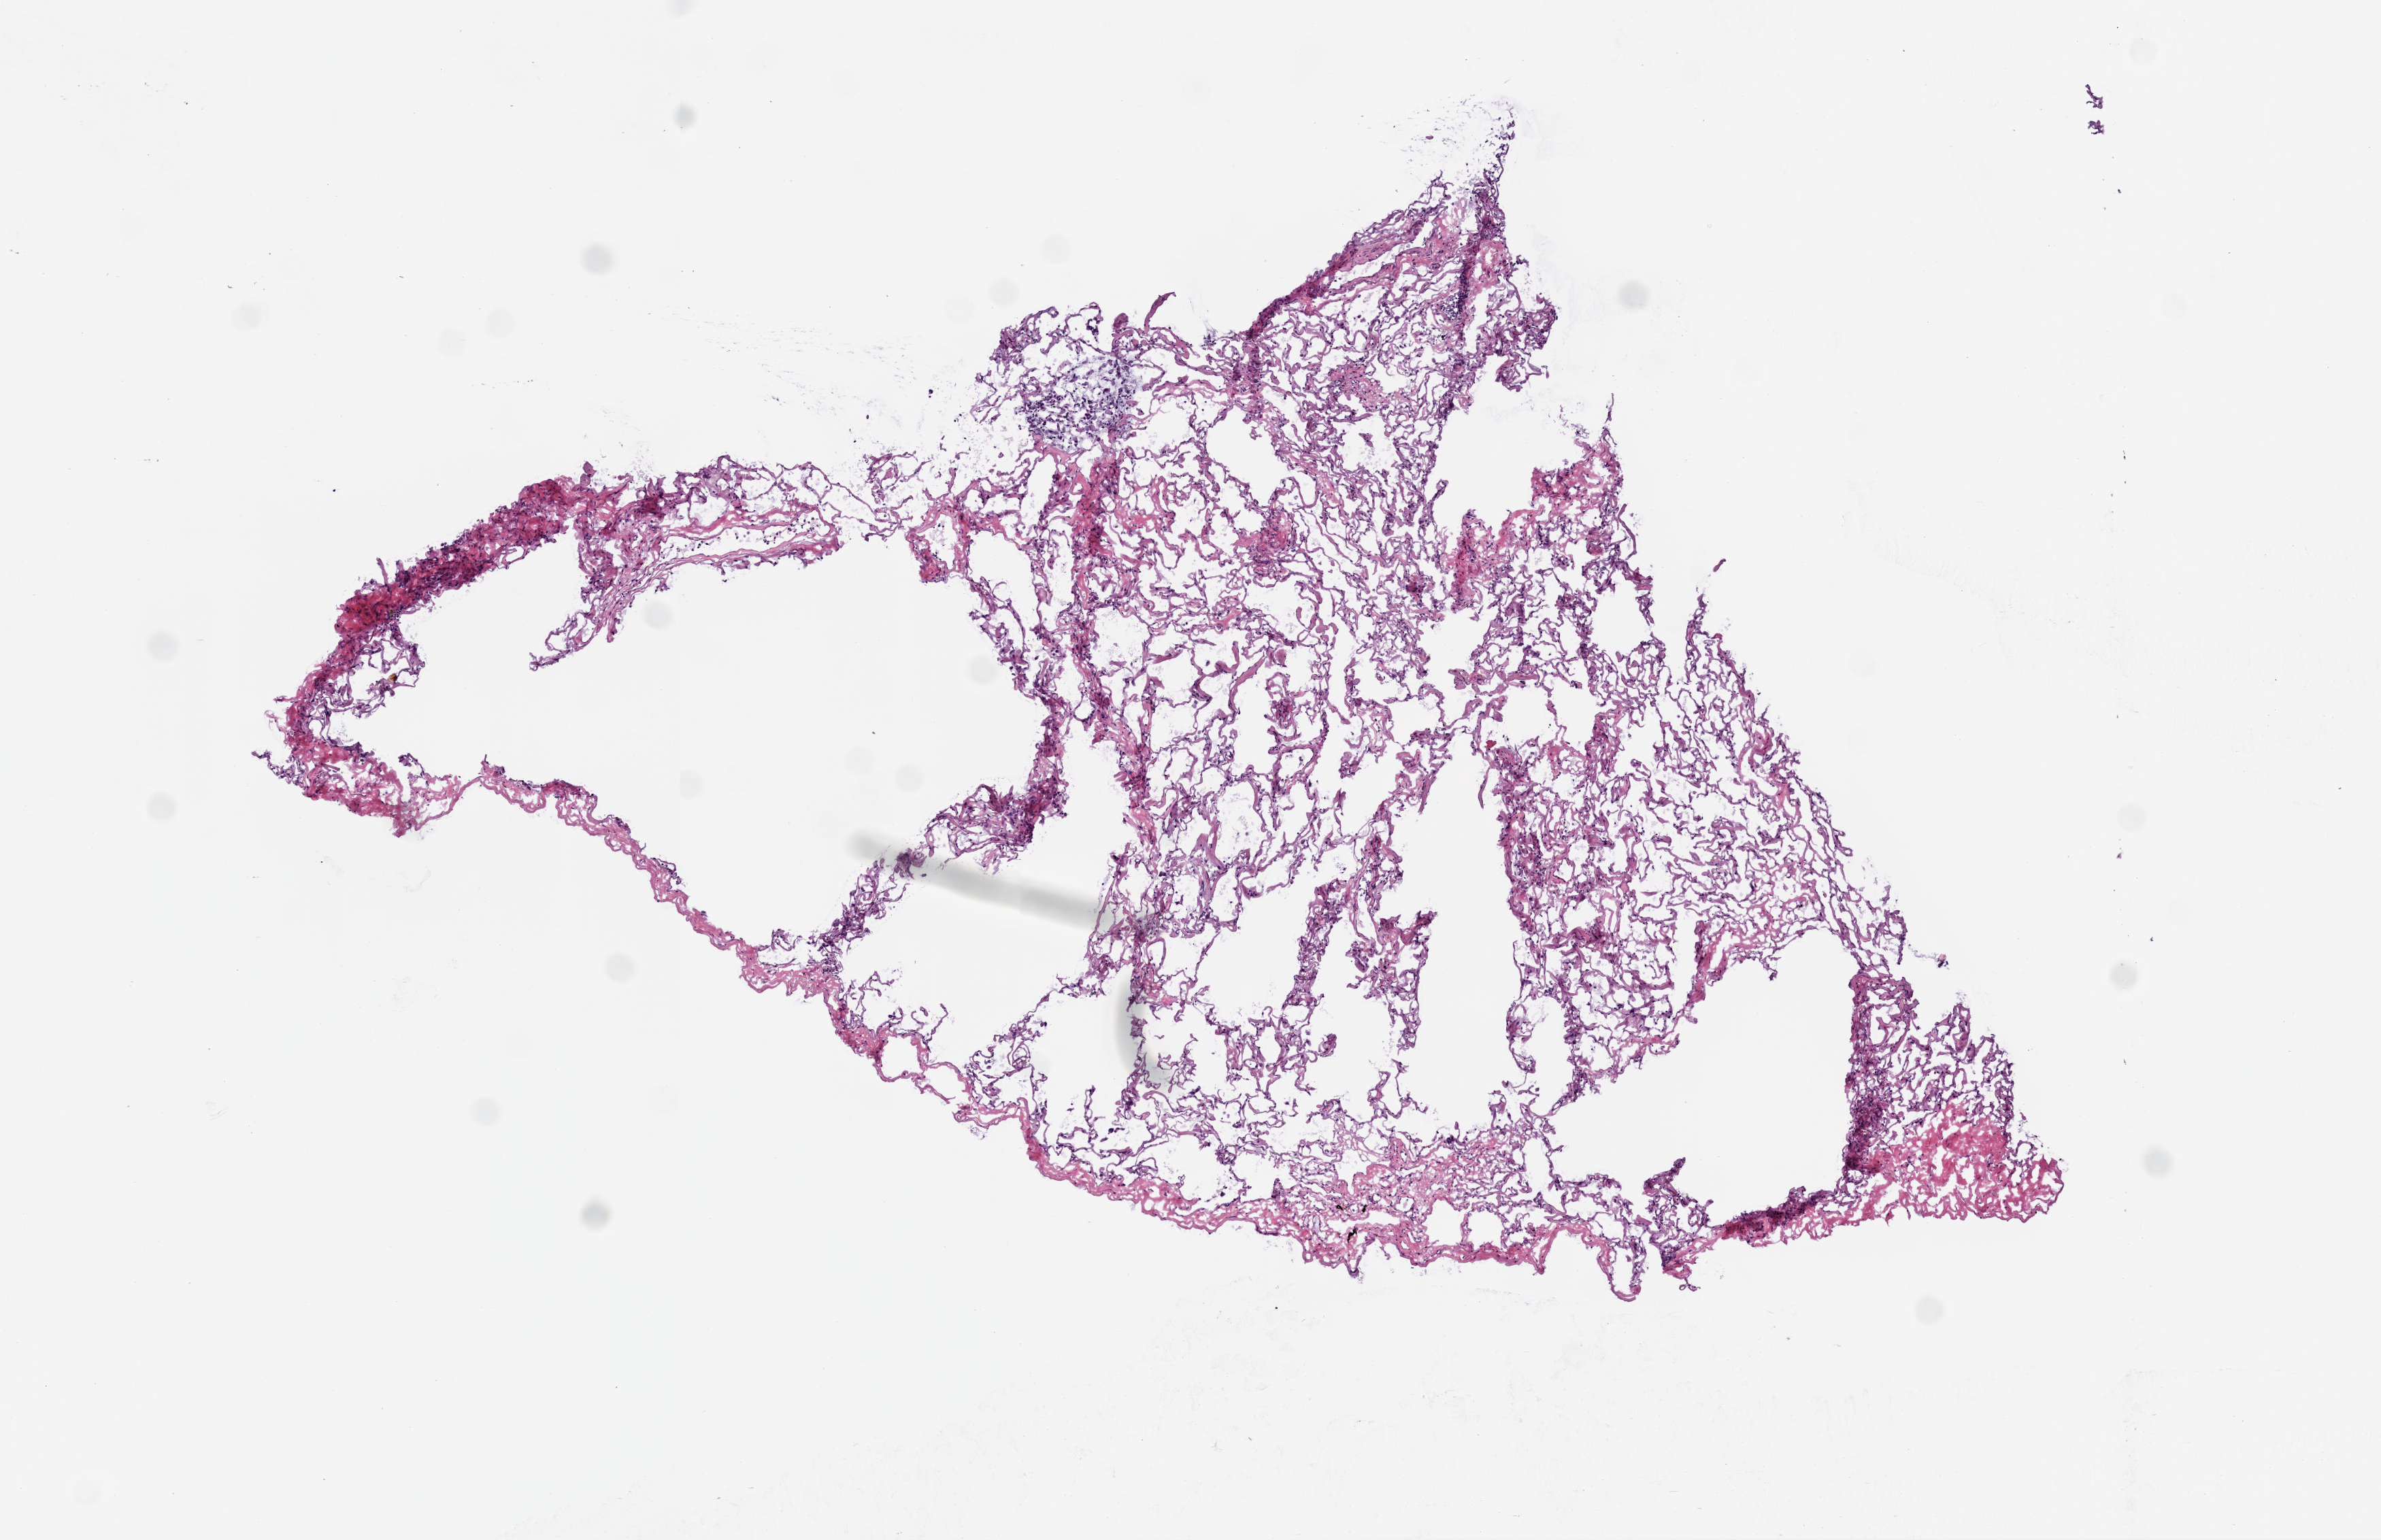
Digitized H&E-stained tissue section (whole slide), a low-resolution overview of the entire scanned area, about 7.0 x 4.5 mm (acquisition: 20x scan); frozen section from the top of the tissue portion; sample: solid tissue normal (non-tumour tissue), lung. Female patient; age at initial diagnosis 65 years.
This section: solid tissue normal (non-tumour) sample from the same patient. Patient diagnosis: Adenocarcinoma, NOS (upper lobe, lung).